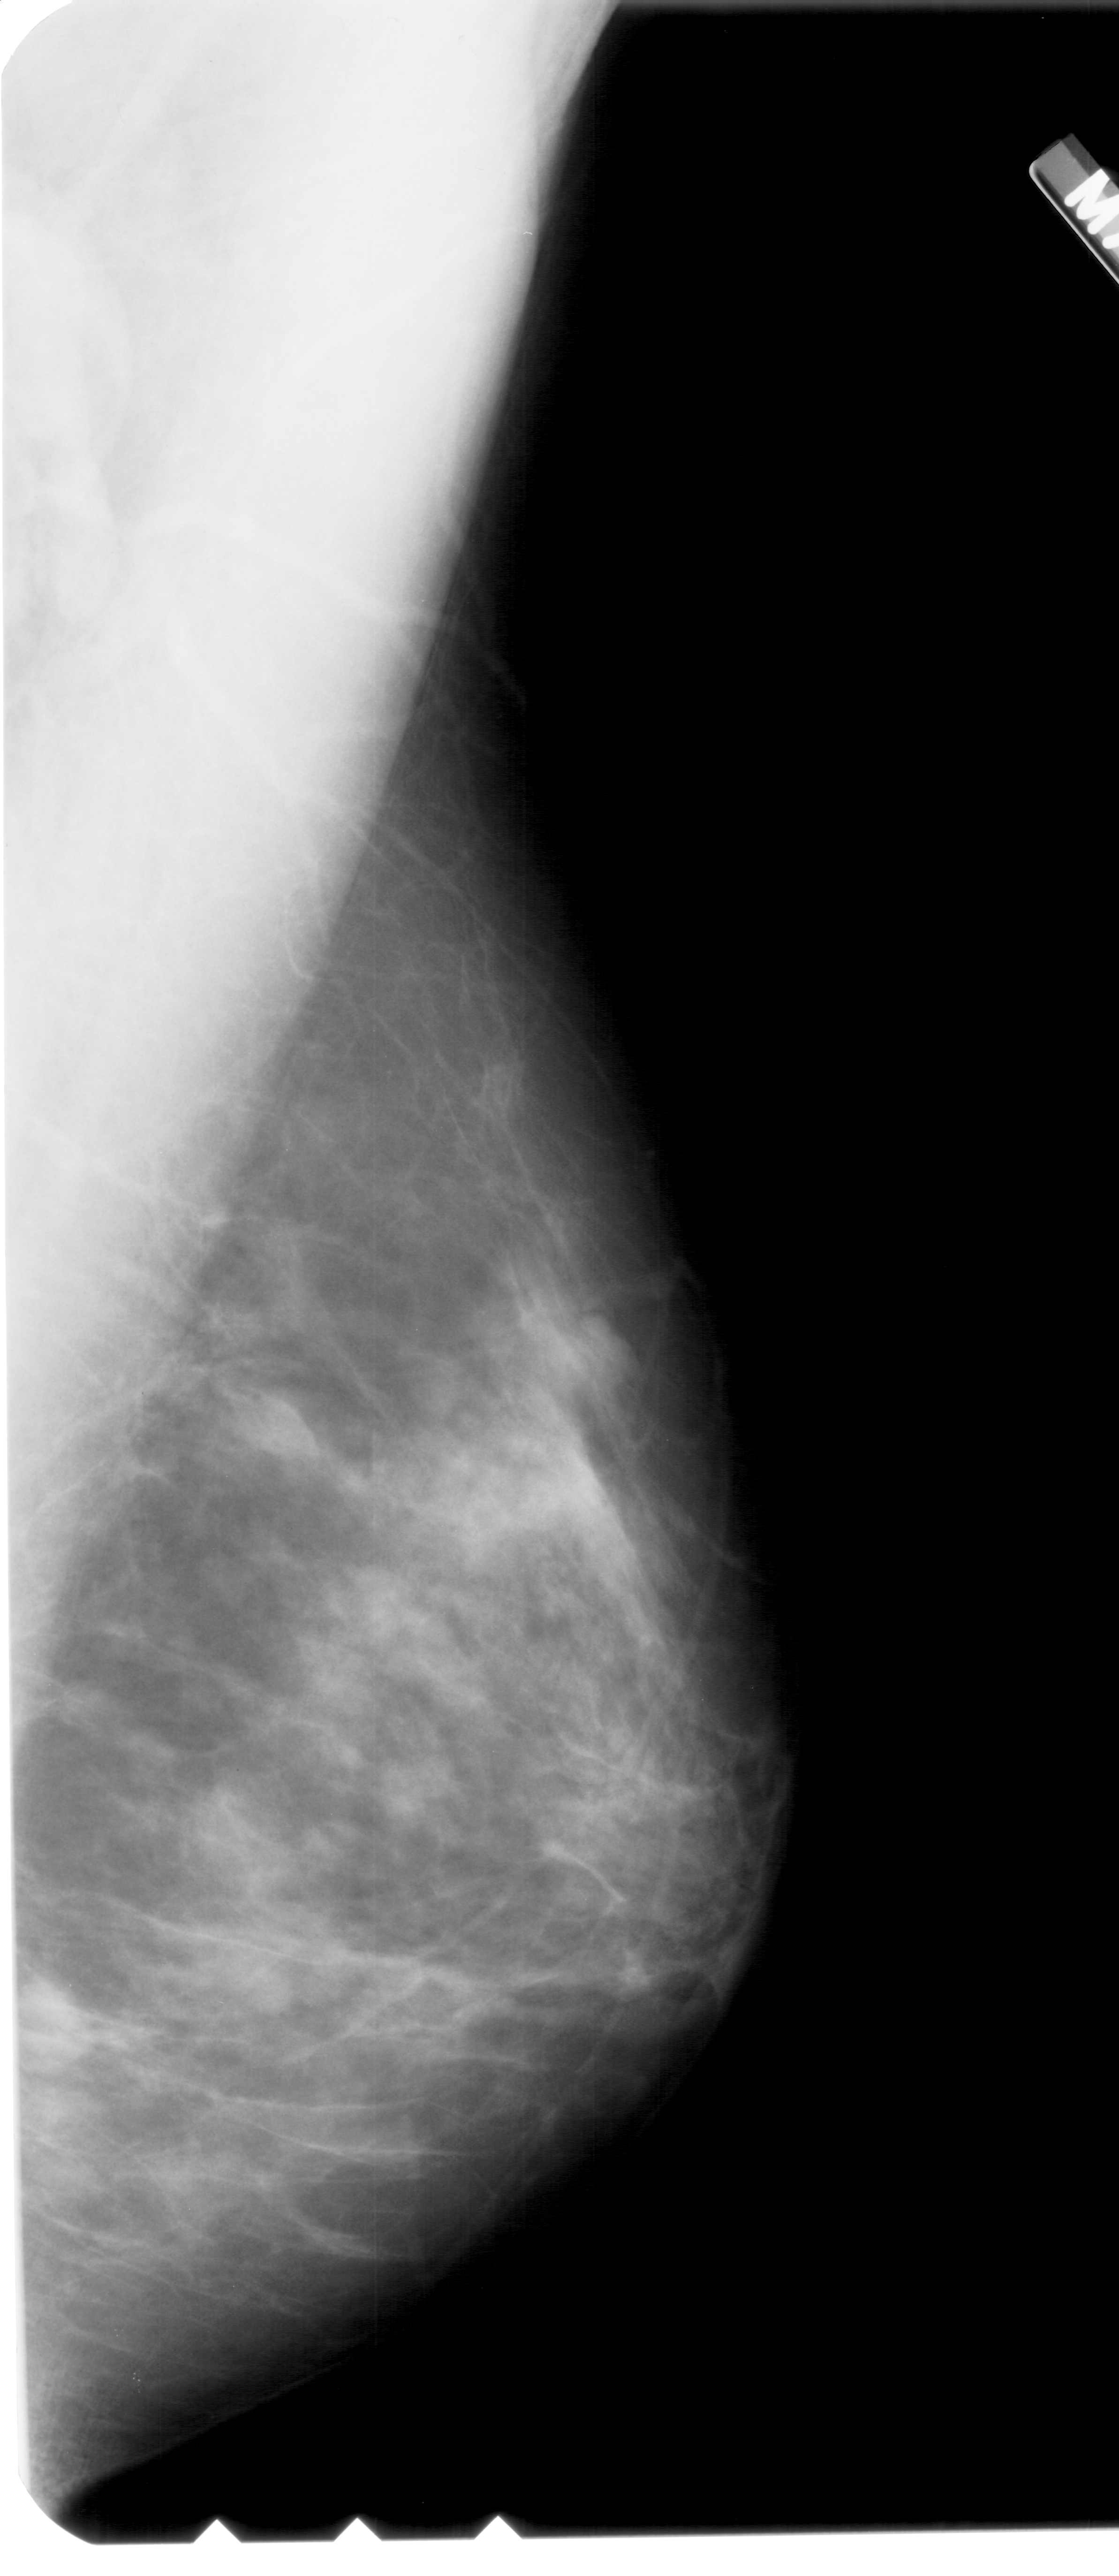
Digitized screen-film mammogram; right breast; MLO view; BI-RADS breast density category 3 (scale 1–4).
Abnormality record for this image: mass, shape lobulated, margins obscured; BI-RADS assessment category 3; subtlety rating 3 on a 1 (subtle) to 5 (obvious) scale; pathology (as recorded): benign.